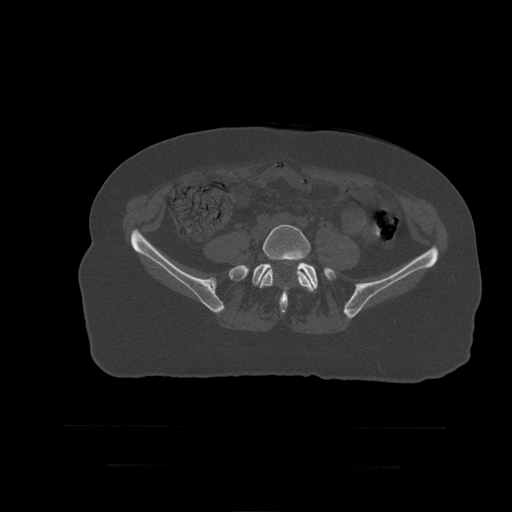
CT including the spine, one axial slice. Position 65 of 399 along the scan axis. Bone window (W 1800 / L 400 HU). 1.25 mm slice thickness. 512 × 512 image matrix, field of view 450 × 450 mm. Patient age 41 years. Case-level facts recorded for this patient, not image findings: primary cancer: breast.
Structures marked on this image (semi-automatic segmentation, software-assisted and operator-edited):
- L5 vertebra: bounding box (x1, y1, x2, y2) in pixels: (259, 225, 316, 292)